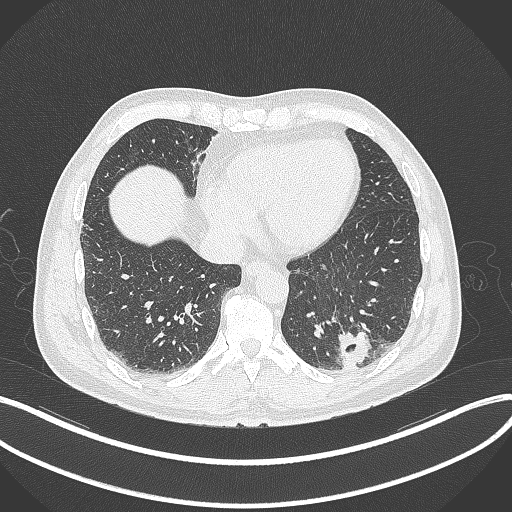
Chest CT, one axial slice. Slice 82 of 300 in the series (ordered by position). Reconstruction kernel B70f. Lung window (W 1500 / L -600 HU). 1 mm slice thickness. 512 × 512 image matrix. Male patient, age 54 years. From the clinical record (not read from this slice): clinical TNM (as recorded): T1c N0 M1; histopathological grade: G3.
Annotated regions visible in this slice (bounding box drawn by a radiologist):
- lung tumour (recorded histology: adenocarcinoma): bounding box <330,325,369,370> (left, top, right, bottom; pixels)